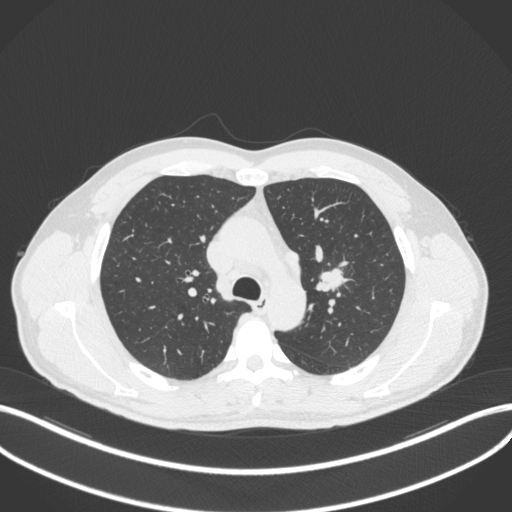
Chest CT, one axial slice; slice 297 of 383 in the series (ordered by position); reconstruction kernel B31f; lung window (W 1500 / L -600 HU); 512 × 512 image matrix, field of view 400 × 400 mm. Male patient, age 50 years. From the clinical record (not read from this slice): clinical TNM (as recorded): T1c N1 M1b.
Annotated regions visible in this slice (bounding box drawn by a radiologist):
- lung tumour (recorded histology: squamous cell carcinoma): bounding box (x1, y1, x2, y2) in pixels: (315, 266, 352, 296)